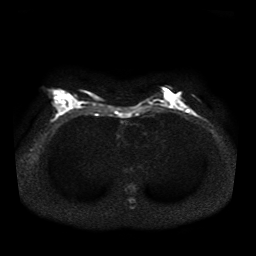
Breast MRI, one axial slice; diffusion-weighted series; image 2 of 4 stored at this slice position (different b-values; order by instance number); 1.5 T; 5 mm slice thickness; 256 × 256 image matrix, field of view 330 × 330 mm. Female patient.
Structures marked on this image (outlined manually by an expert reader):
- tumour on diffusion-weighted imaging: bounding box <191,112,194,115> (left, top, right, bottom; pixels)